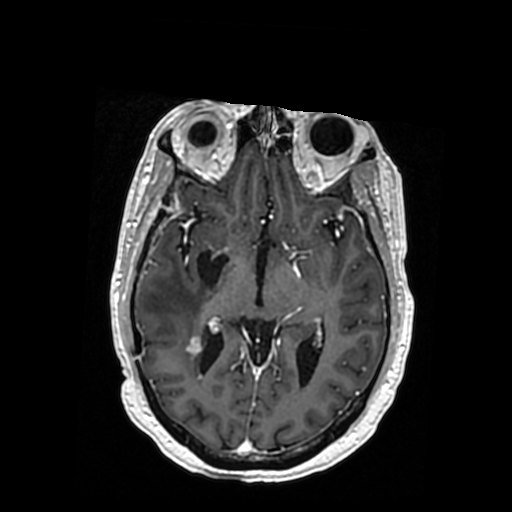
Brain MRI from a brain-tumour surgery series, one axial slice. Position 197 of 364 along the scan axis. T1-weighted post-contrast. 0.5 mm slice thickness. 512 × 512 image matrix, field of view 260 × 260 mm. From the clinical record (not read from this slice): histopathology: Oligodendroglioma; WHO grade: 3; IDH mutation: yes; tumour location: Right Posterior Temporal Inferior Parietal.
Annotated regions visible in this slice (expert manual segmentation):
- previous resection cavity: bounding box <197,252,228,285> (left, top, right, bottom; pixels)
- tumour: <191,333,206,350>